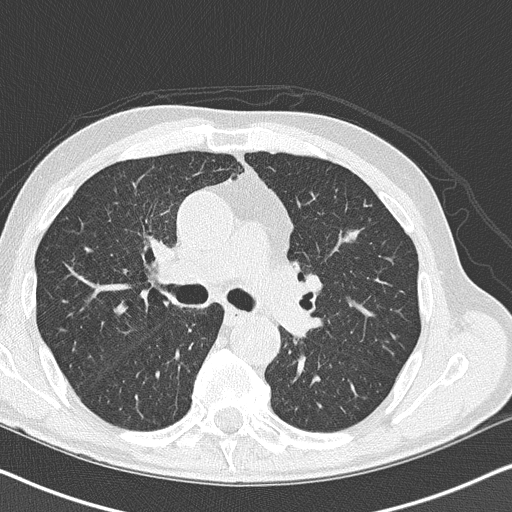
Chest CT (low-dose screening protocol), one axial image; second annual screen; lung window (W 1500 / L -600 HU); lung (sharp) reconstruction kernel (B50f); slice 98 of 158 in the series. Male participant, aged 73 years at enrolment. Current smoker at enrolment.
Expert reader's lesion annotation, bounding box [x1, y1, x2, y2] px = [317, 219, 377, 270]. The screening reader recorded 3 non-calcified nodules or masses ≥4 mm on this exam; which of them this box marks is not recorded. Official screen result: positive, other. Participant outcome: lung cancer diagnosed 36 days after this screen — small cell carcinoma, NOS, left upper lobe, stage IIIB (AJCC 6th edition), 19 mm at pathology.